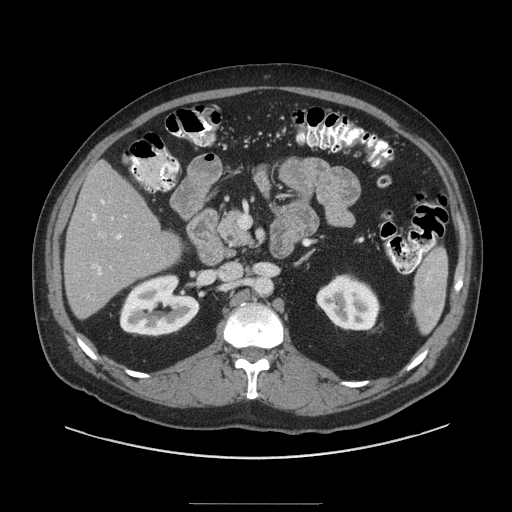
Contrast-enhanced abdominal CT (liver protocol), one axial slice. Slice 43 of 91 in the series (ordered by position). Reconstruction kernel STANDARD. Soft-tissue window (W 400 / L 40 HU). 2.5 mm slice thickness. 512 × 512 image matrix. Case-level facts recorded for this patient, not image findings: diagnosis: hepatocellular carcinoma (patient treated with transarterial chemoembolisation; whether this scan precedes or follows treatment is not stated here); TNM stage (as recorded): Stage-I; Child-Pugh class: A; tumour size: 4 cm.
Structures marked on this image (semi-automatic segmentation, software-assisted and operator-edited):
- liver parenchyma outside the tumour (the mass and vessels are separate outlines, so this box may not span the whole liver): bounding box [x1, y1, x2, y2] px = [64, 160, 180, 318]
- liver vessels: [92, 200, 126, 275]